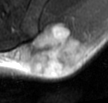
MRI of an extremity soft-tissue mass, one axial slice. Position 23 of 42 along the scan axis. T2-weighted fat-saturated. MR volume resampled by the dataset authors to the PET/CT grid (not the native acquisition matrix). 3.27 mm slice thickness. 108 × 103 image matrix, field of view 105 × 101 mm. Male patient. From the clinical record (not read from this slice): histological type: leiomyosarcoma; grade: intermediate; site of the primary tumour: left pelvis.
Outlined on this slice (expert contour drawn on MRI and transferred to this co-registered scan by the dataset authors):
- gross tumour volume (mass): bounding box [x1, y1, x2, y2] px = [21, 21, 88, 75]